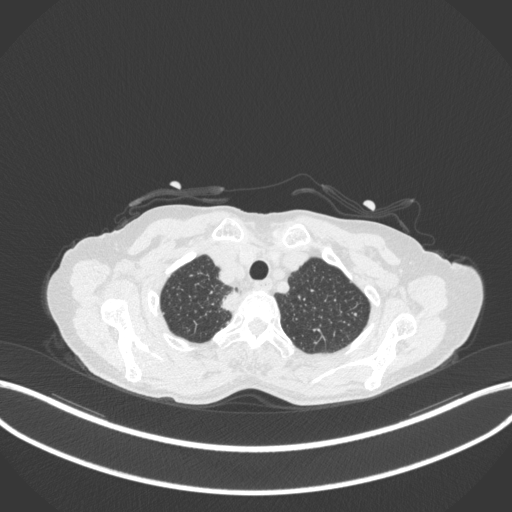
Chest CT, one axial slice. Position 330 of 363 along the scan axis. 120 kVp. Lung window (W 1500 / L -600 HU). 1 mm slice thickness. 512 × 512 image matrix, field of view 400 × 400 mm. Female patient, age 75 years. Case-level facts recorded for this patient, not image findings: clinical TNM (as recorded): T1c N1 M1.
Annotated regions visible in this slice (bounding box drawn by a radiologist):
- lung tumour (recorded histology: adenocarcinoma): bounding box <216,289,244,315> (left, top, right, bottom; pixels)